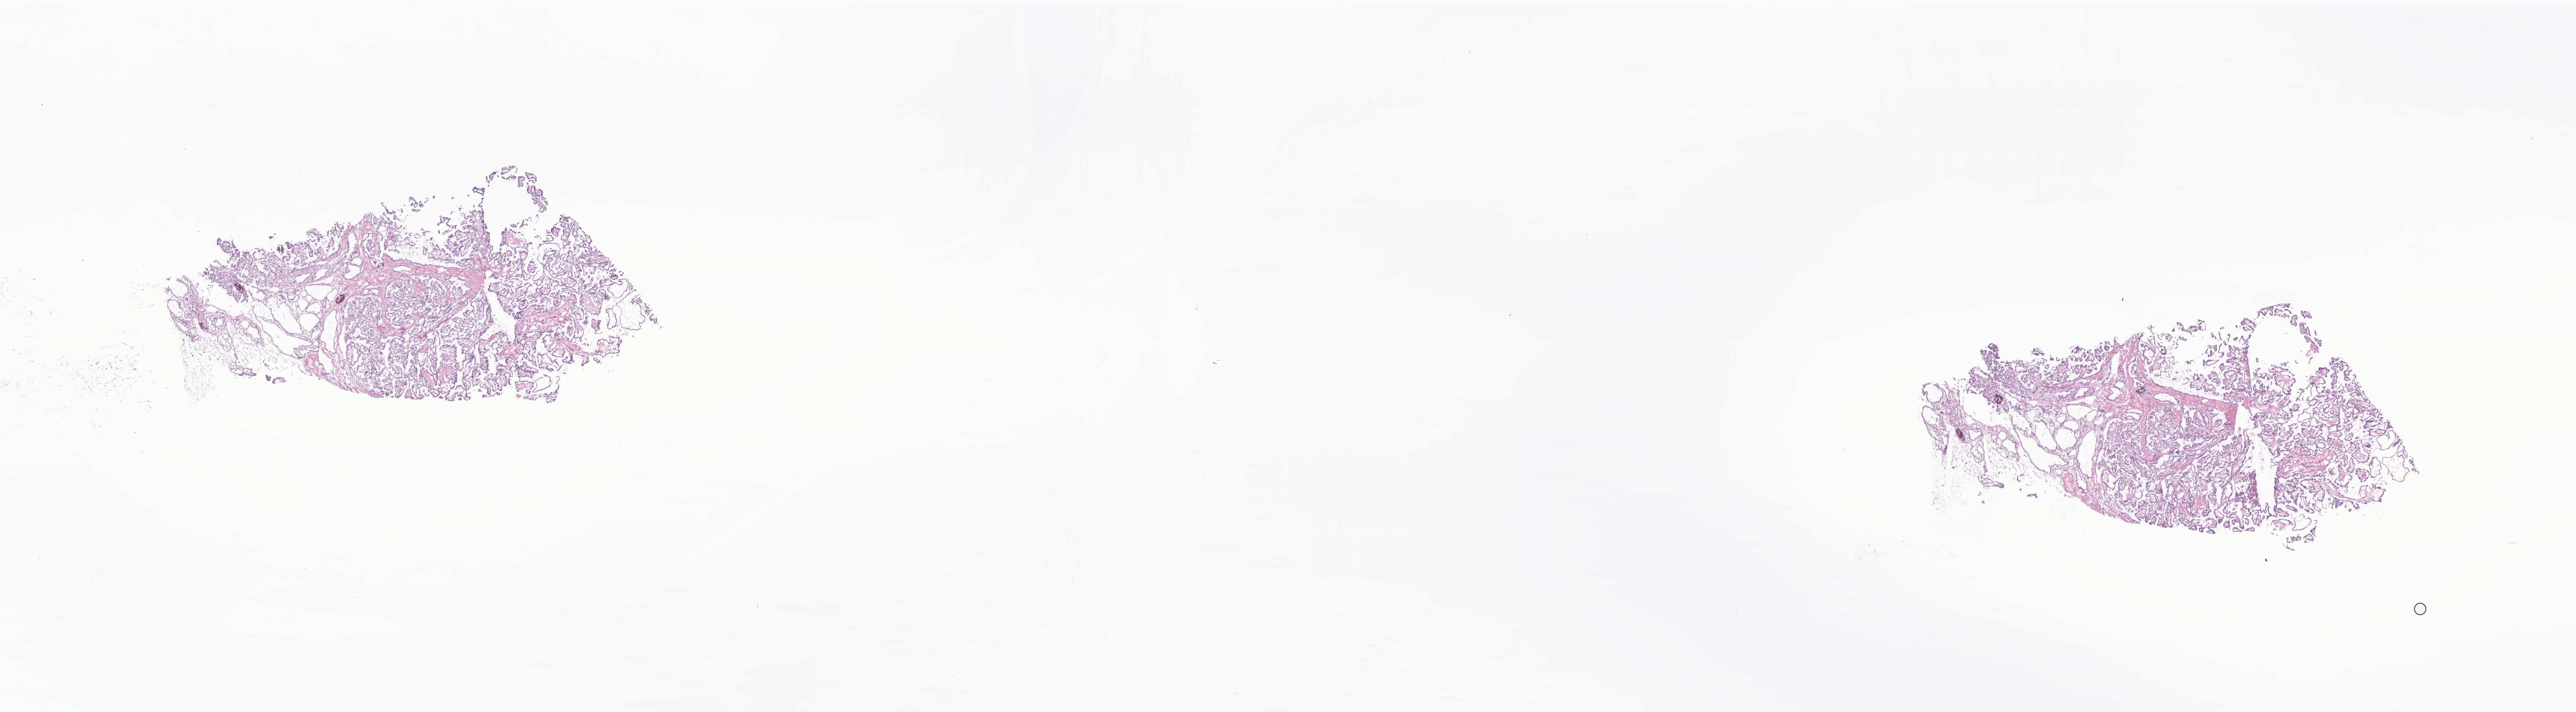
Digitized H&E-stained section of tumor tissue from the thyroid, a low-resolution overview of the entire scanned area, about 29.1 x 8.0 mm; cryosection (OCT / tissue freezing medium). Patient: female, age 205 months (17 years 1 month).
Diagnosis (ICD-O-3 morphology term): Carcinoma, NOS.